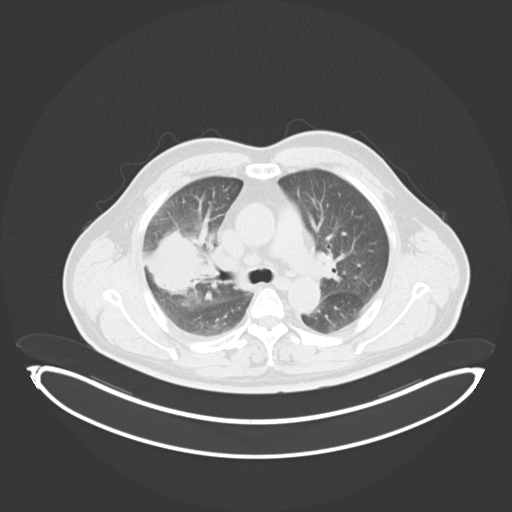
Chest CT, one axial slice; position 217 of 284 along the scan axis; reconstruction kernel B30f; lung window (W 1500 / L -600 HU); 3 mm slice thickness; 512 × 512 image matrix, field of view 500 × 500 mm. Patient: male, 55 years. Case-level facts recorded for this patient, not image findings: clinical TNM (as recorded): T3 N2 M1.
Annotated regions visible in this slice (rectangle marked by the reading radiologist):
- lung tumour (recorded histology: adenocarcinoma): box from (x=138, y=226) to (x=218, y=300) px